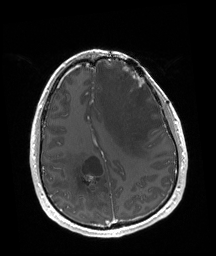
Brain MRI from a brain-tumour surgery series, one axial slice. Position 62 of 192 along the scan axis. T1-weighted post-contrast. 1 mm slice thickness. 216 × 256 image matrix, field of view 219 × 260 mm. Case-level facts recorded for this patient, not image findings: tumour location: Left Frontal.
Outlined on this slice (manually delineated by an expert):
- tumour: bounding box (x1, y1, x2, y2) in pixels: (122, 65, 145, 88)